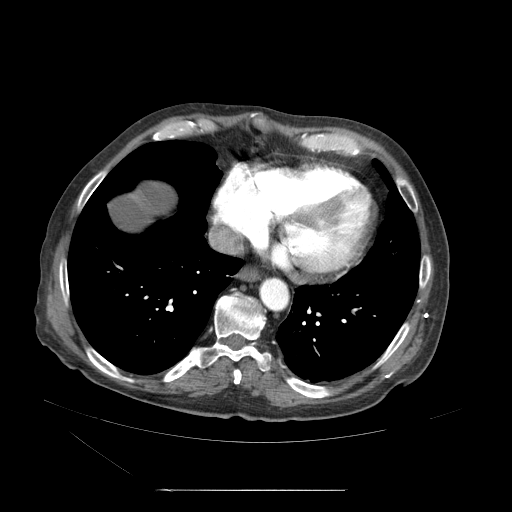
Contrast-enhanced abdominal CT (liver protocol), one axial slice; slice 61 of 71 in the series (ordered by position); reconstruction kernel STANDARD; soft-tissue window (W 400 / L 40 HU); 2.5 mm slice thickness; 512 × 512 image matrix, field of view 440 × 440 mm. Case-level facts recorded for this patient, not image findings: diagnosis: hepatocellular carcinoma (patient treated with transarterial chemoembolisation; whether this scan precedes or follows treatment is not stated here); TNM stage (as recorded): Stage-II; Child-Pugh class: A; tumour nodularity: multinodular; tumour size: 1 cm.
Structures marked on this image (semi-automatic segmentation, software-assisted and operator-edited):
- abdominal aorta: box from (x=260, y=275) to (x=289, y=312) px
- liver parenchyma outside the tumour (the mass and vessels are separate outlines, so this box may not span the whole liver): (x=149, y=182)–(x=182, y=224)